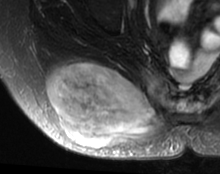
MRI of an extremity soft-tissue mass, one axial slice. Slice 27 of 63 in the series (ordered by position). T2-weighted fat-saturated. MR volume resampled by the dataset authors to the PET/CT grid (not the native acquisition matrix). 3.27 mm slice thickness. 220 × 174 image matrix, field of view 215 × 170 mm. Female patient. Case-level facts recorded for this patient, not image findings: histological type: spindle cell suggestive of myxofibrosarcoma; grade: intermediate; site of the primary tumour: right buttock.
Structures marked on this image (expert contour drawn on MRI and transferred to this co-registered scan by the dataset authors):
- gross tumour volume (mass): bounding box [x1, y1, x2, y2] px = [47, 61, 164, 147]